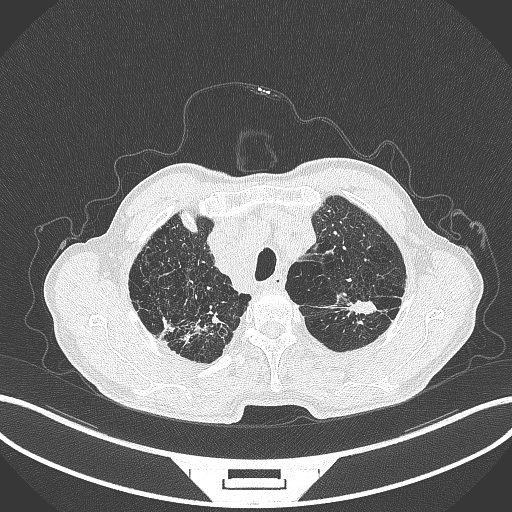
Chest CT, one axial slice; position 378 of 463 along the scan axis; reconstruction kernel B70f; 120 kVp; lung window (W 1500 / L -600 HU); 1 mm slice thickness; 512 × 512 image matrix, field of view 400 × 400 mm. Male patient, age 74 years. Case-level facts recorded for this patient, not image findings: clinical TNM (as recorded): T2a N1 M0.
Outlined on this slice (bounding box drawn by a radiologist):
- lung tumour (recorded histology: adenocarcinoma): bounding box (x1, y1, x2, y2) in pixels: (337, 294, 381, 320)